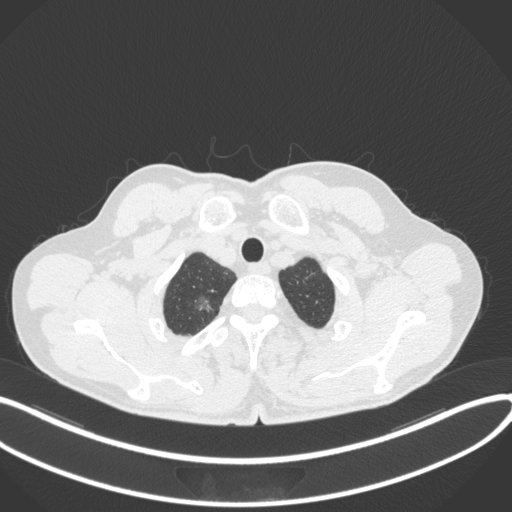
Chest CT, one axial slice. Position 353 of 407 along the scan axis. Reconstruction kernel B31f. 120 kVp. Lung window (W 1500 / L -600 HU). 1 mm slice thickness. 512 × 512 image matrix. Patient: male, 58 years. Case-level facts recorded for this patient, not image findings: clinical TNM (as recorded): T1c N0 M0.
Structures marked on this image (rectangle marked by the reading radiologist):
- lung tumour (recorded histology: adenocarcinoma): box from (x=189, y=296) to (x=212, y=317) px